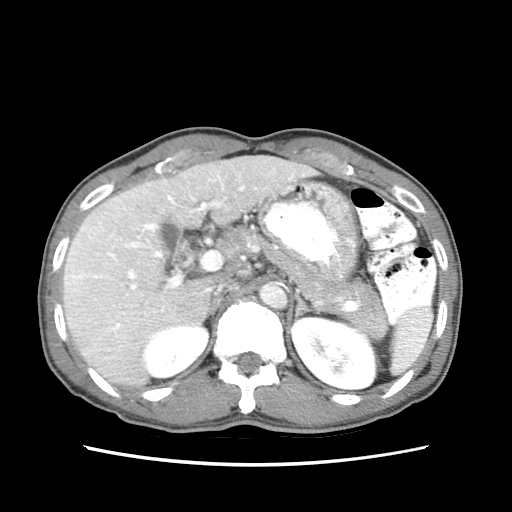
Contrast-enhanced abdominal CT (liver protocol), one axial slice. Position 42 of 79 along the scan axis. Soft-tissue window (W 400 / L 40 HU). 2.5 mm slice thickness. 512 × 512 image matrix, field of view 320 × 320 mm. Case-level facts recorded for this patient, not image findings: diagnosis: hepatocellular carcinoma (patient treated with transarterial chemoembolisation; whether this scan precedes or follows treatment is not stated here); TNM stage (as recorded): Stage-IIIB; Child-Pugh class: A.
Structures marked on this image (semi-automatic segmentation, software-assisted and operator-edited):
- liver parenchyma outside the tumour (the mass and vessels are separate outlines, so this box may not span the whole liver): bounding box (x1, y1, x2, y2) in pixels: (63, 154, 318, 388)
- mass: (64, 236, 116, 288)
- liver vessels: (72, 162, 294, 340)